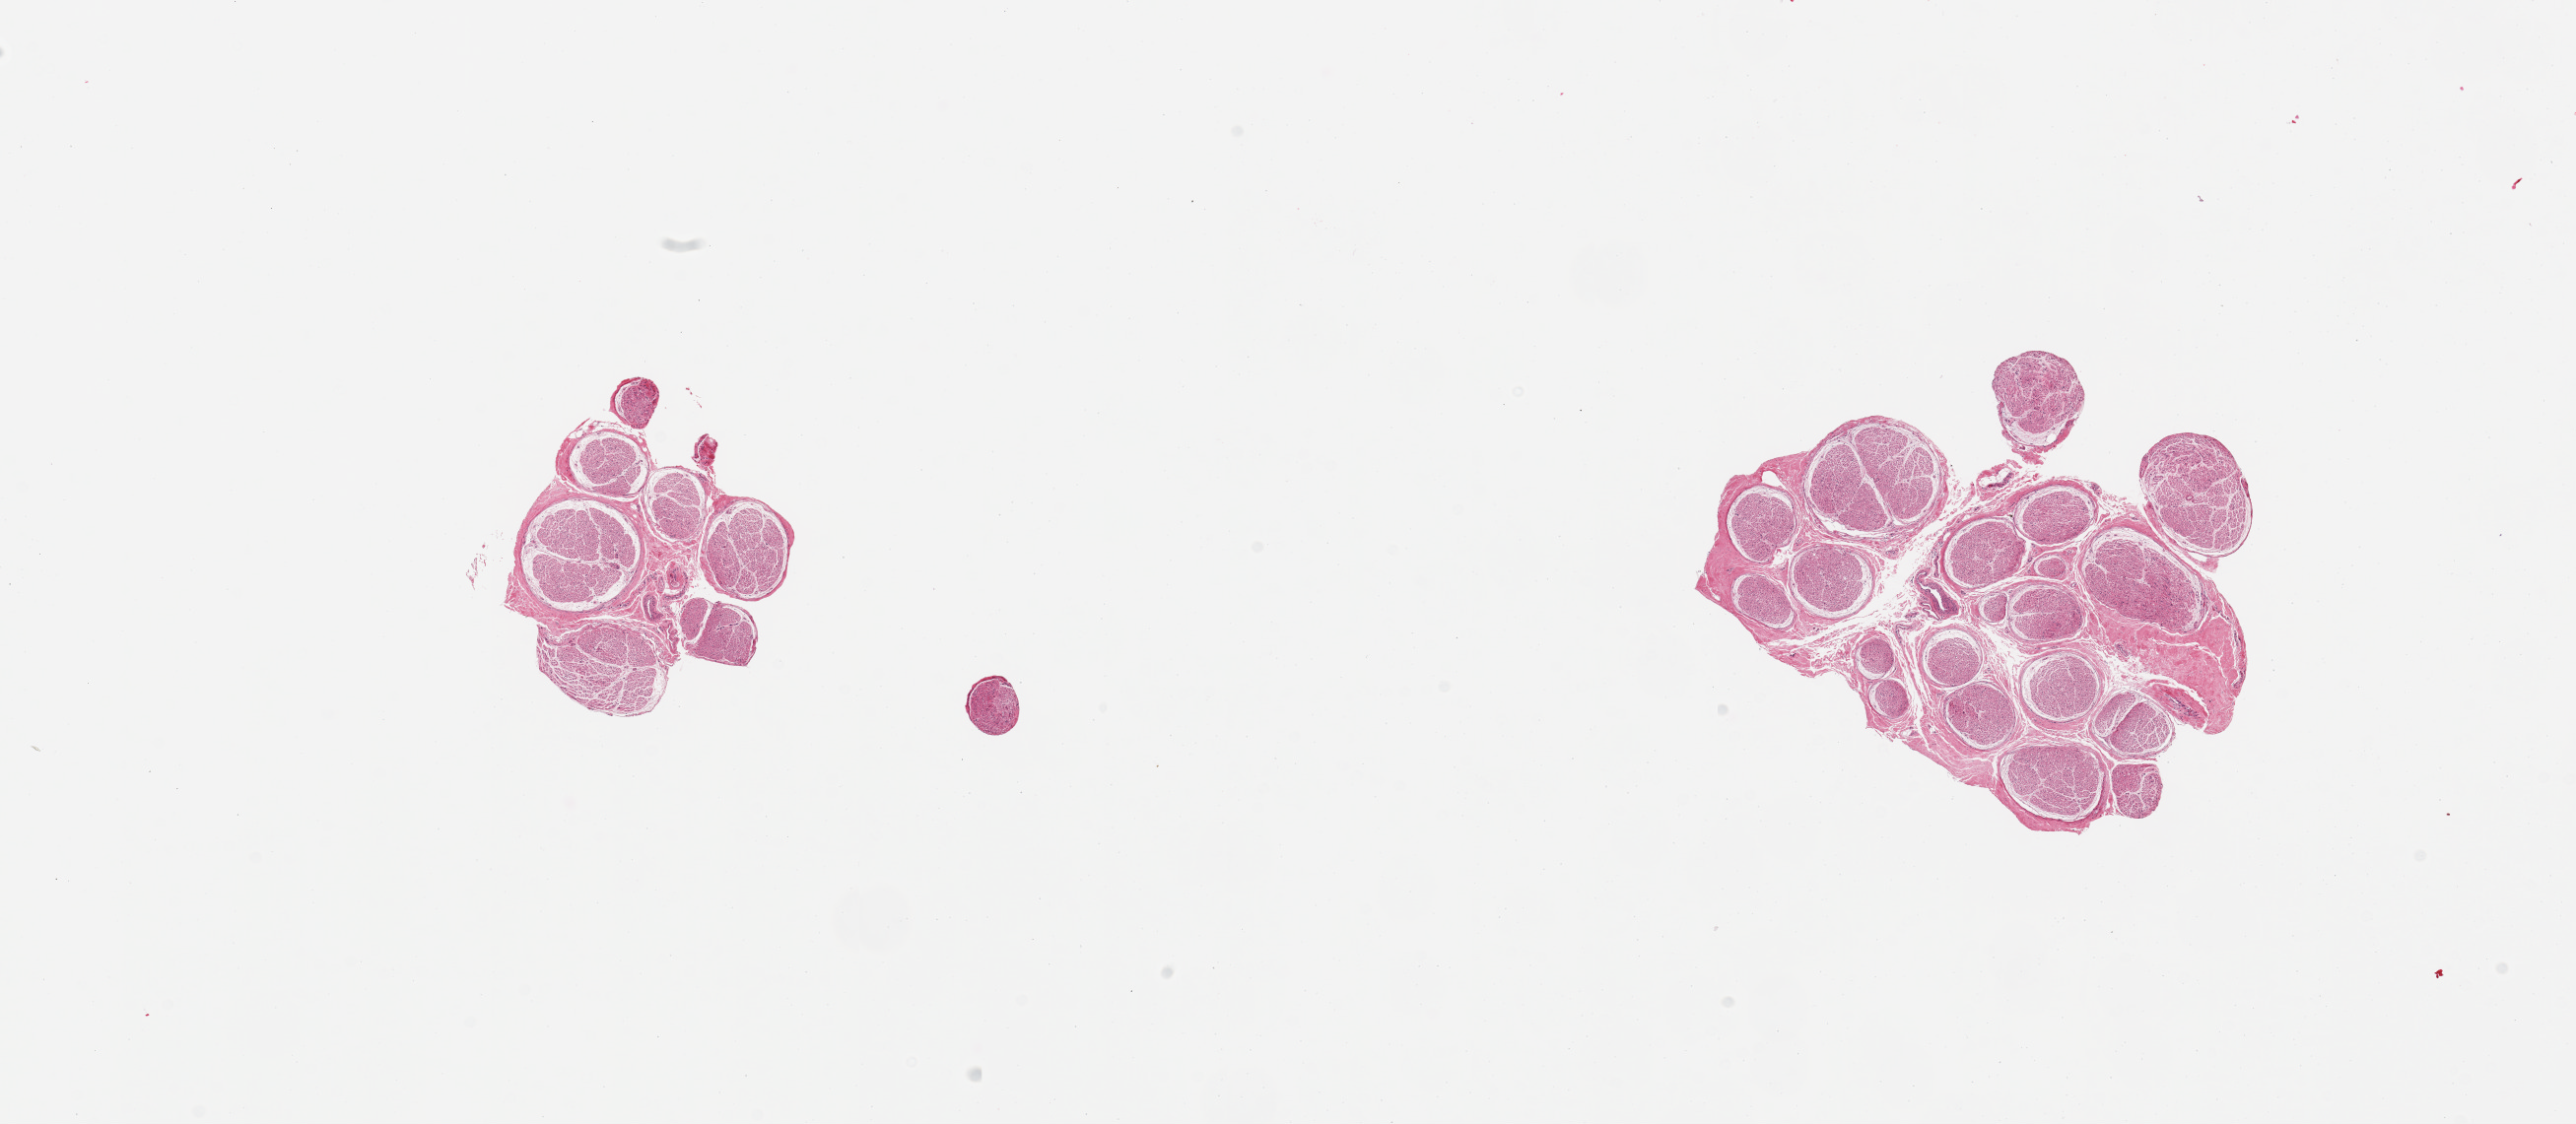
Haematoxylin and eosin whole-slide image — whole scanned area (about 20.7 x 9.0 mm) shown as a low-resolution overview. PAXgene-fixed, paraffin-embedded tissue. Sampled site (target tissue): tibial nerve. Tissue donor sample. Donor sex: male.
Pathologist's review note for this sample: 2 pieces; well trimmed.